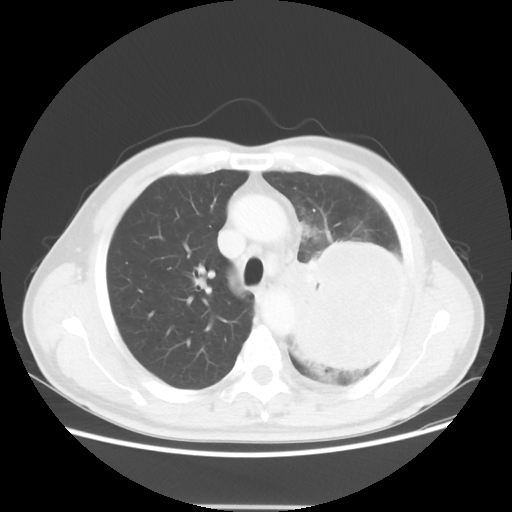
Chest CT, one axial slice. Slice 38 of 53 in the series (ordered by position). 100 kVp. Lung window (W 1500 / L -600 HU). 512 × 512 image matrix. Male patient, age 60 years. From the clinical record (not read from this slice): clinical TNM (as recorded): T4 N1 M1a; histopathological grade: G3.
Structures marked on this image (rectangle marked by the reading radiologist):
- lung tumour (recorded histology: large cell carcinoma): bounding box [x1, y1, x2, y2] px = [302, 240, 419, 373]